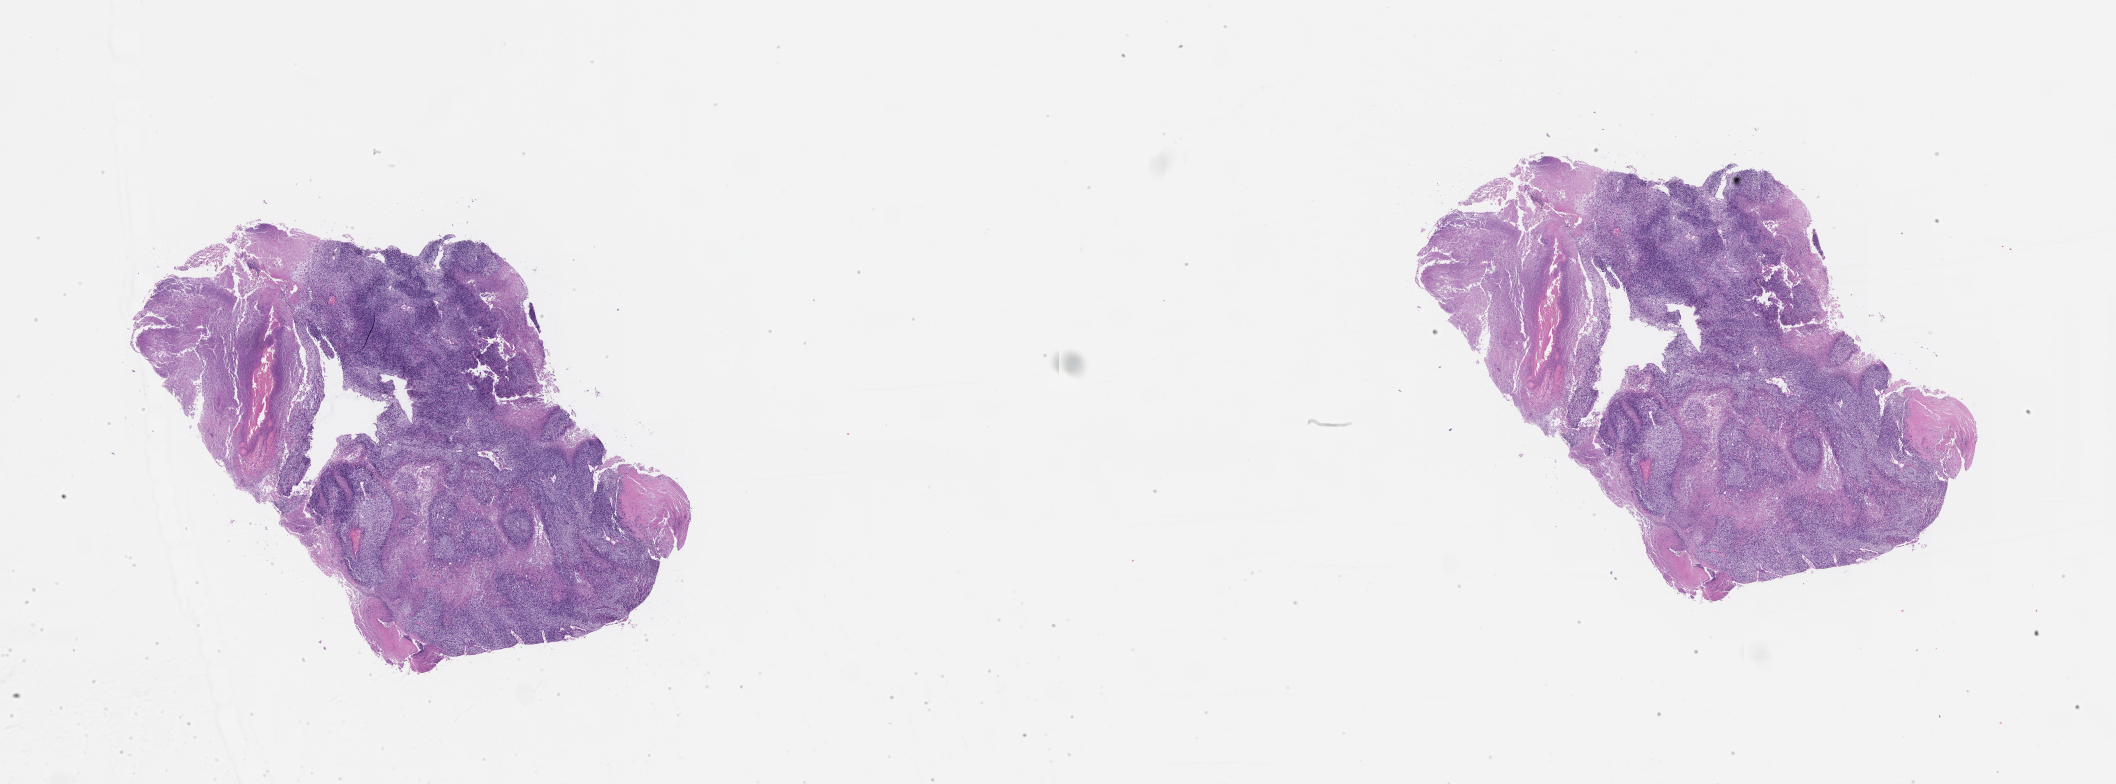
Whole-slide histology image, H&E-stained, shown as a low-resolution overview of the whole scanned area (about 34.1 x 12.6 mm, slide scanned at 20x).
Patient diagnosis (cohort enrolment): sarcoma (site not recorded at cohort level).